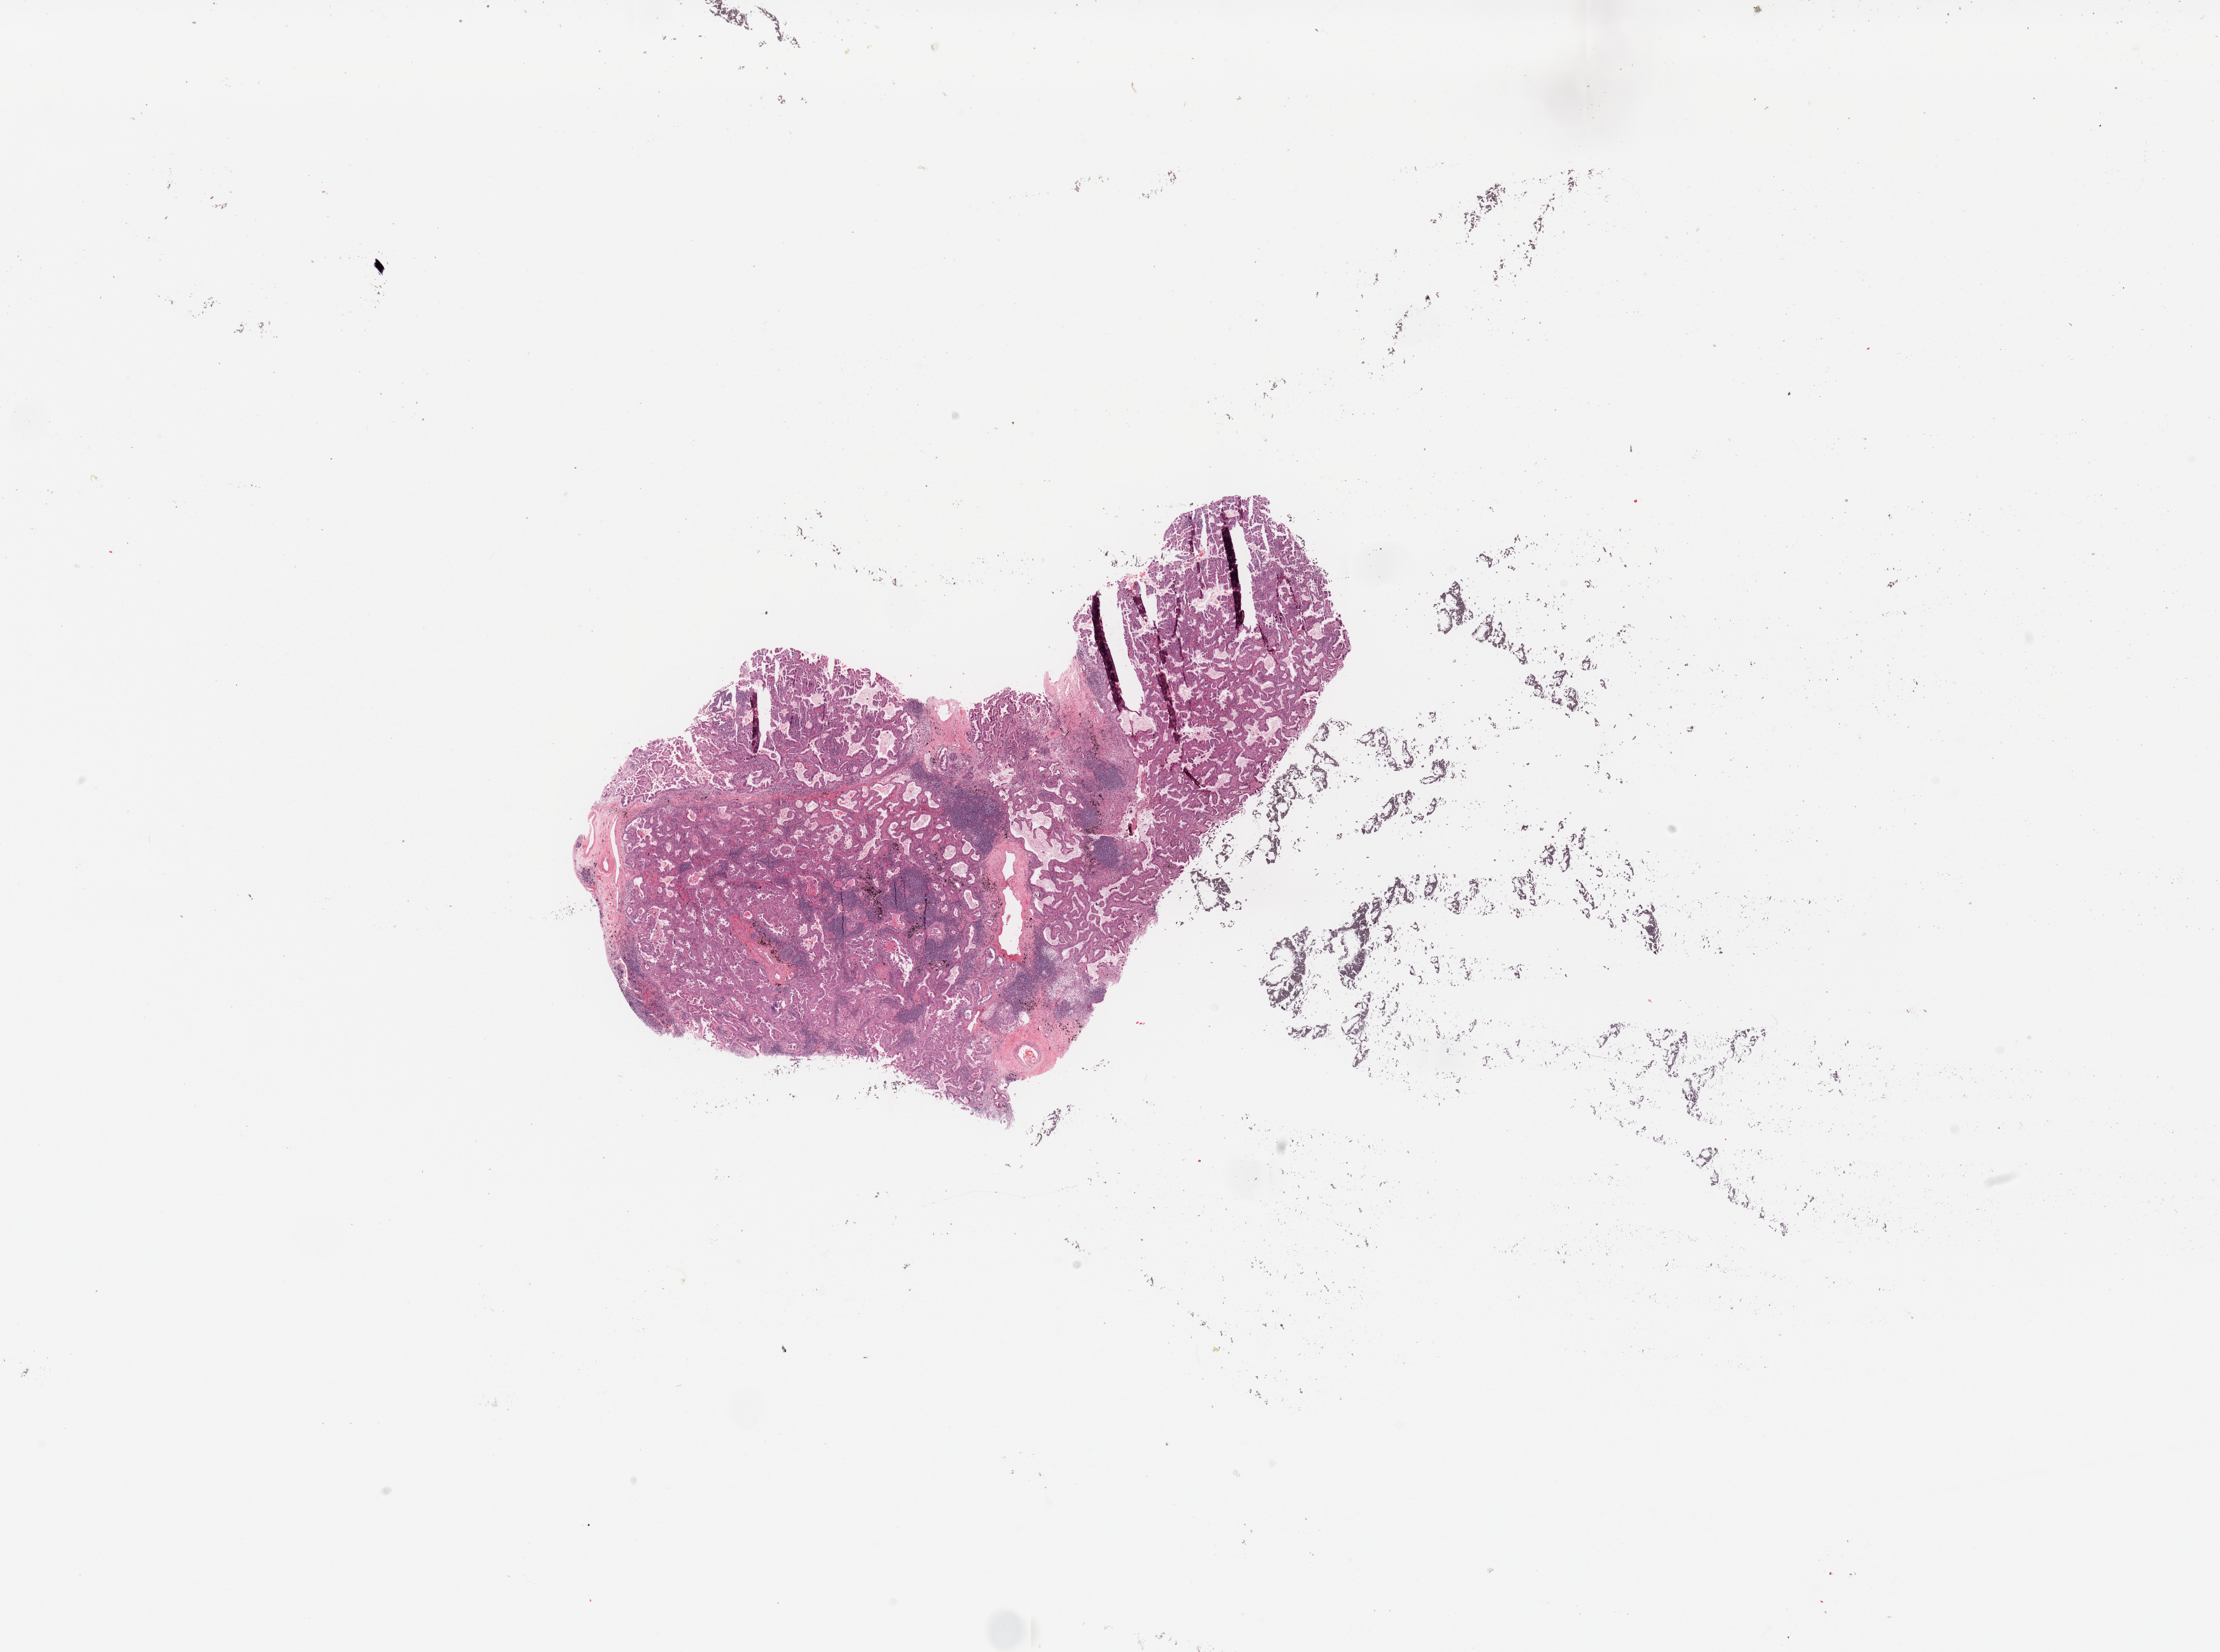
Whole-slide histology image, H&E — shown as a low-resolution overview of the whole scanned area (about 27.6 x 20.5 mm, acquisition: 20x scan); tumour tissue sample, sampled site: lung. 68-year-old male patient. Histologic grade: G2 (moderately differentiated). Pathologist review of this section (percent, as recorded): tumour nuclei 55%, necrosis 5%.
- AJCC pathologic stage: IA
- diagnosis: Adenocarcinoma, NOS
- primary tumour site (as recorded): right lower lobe